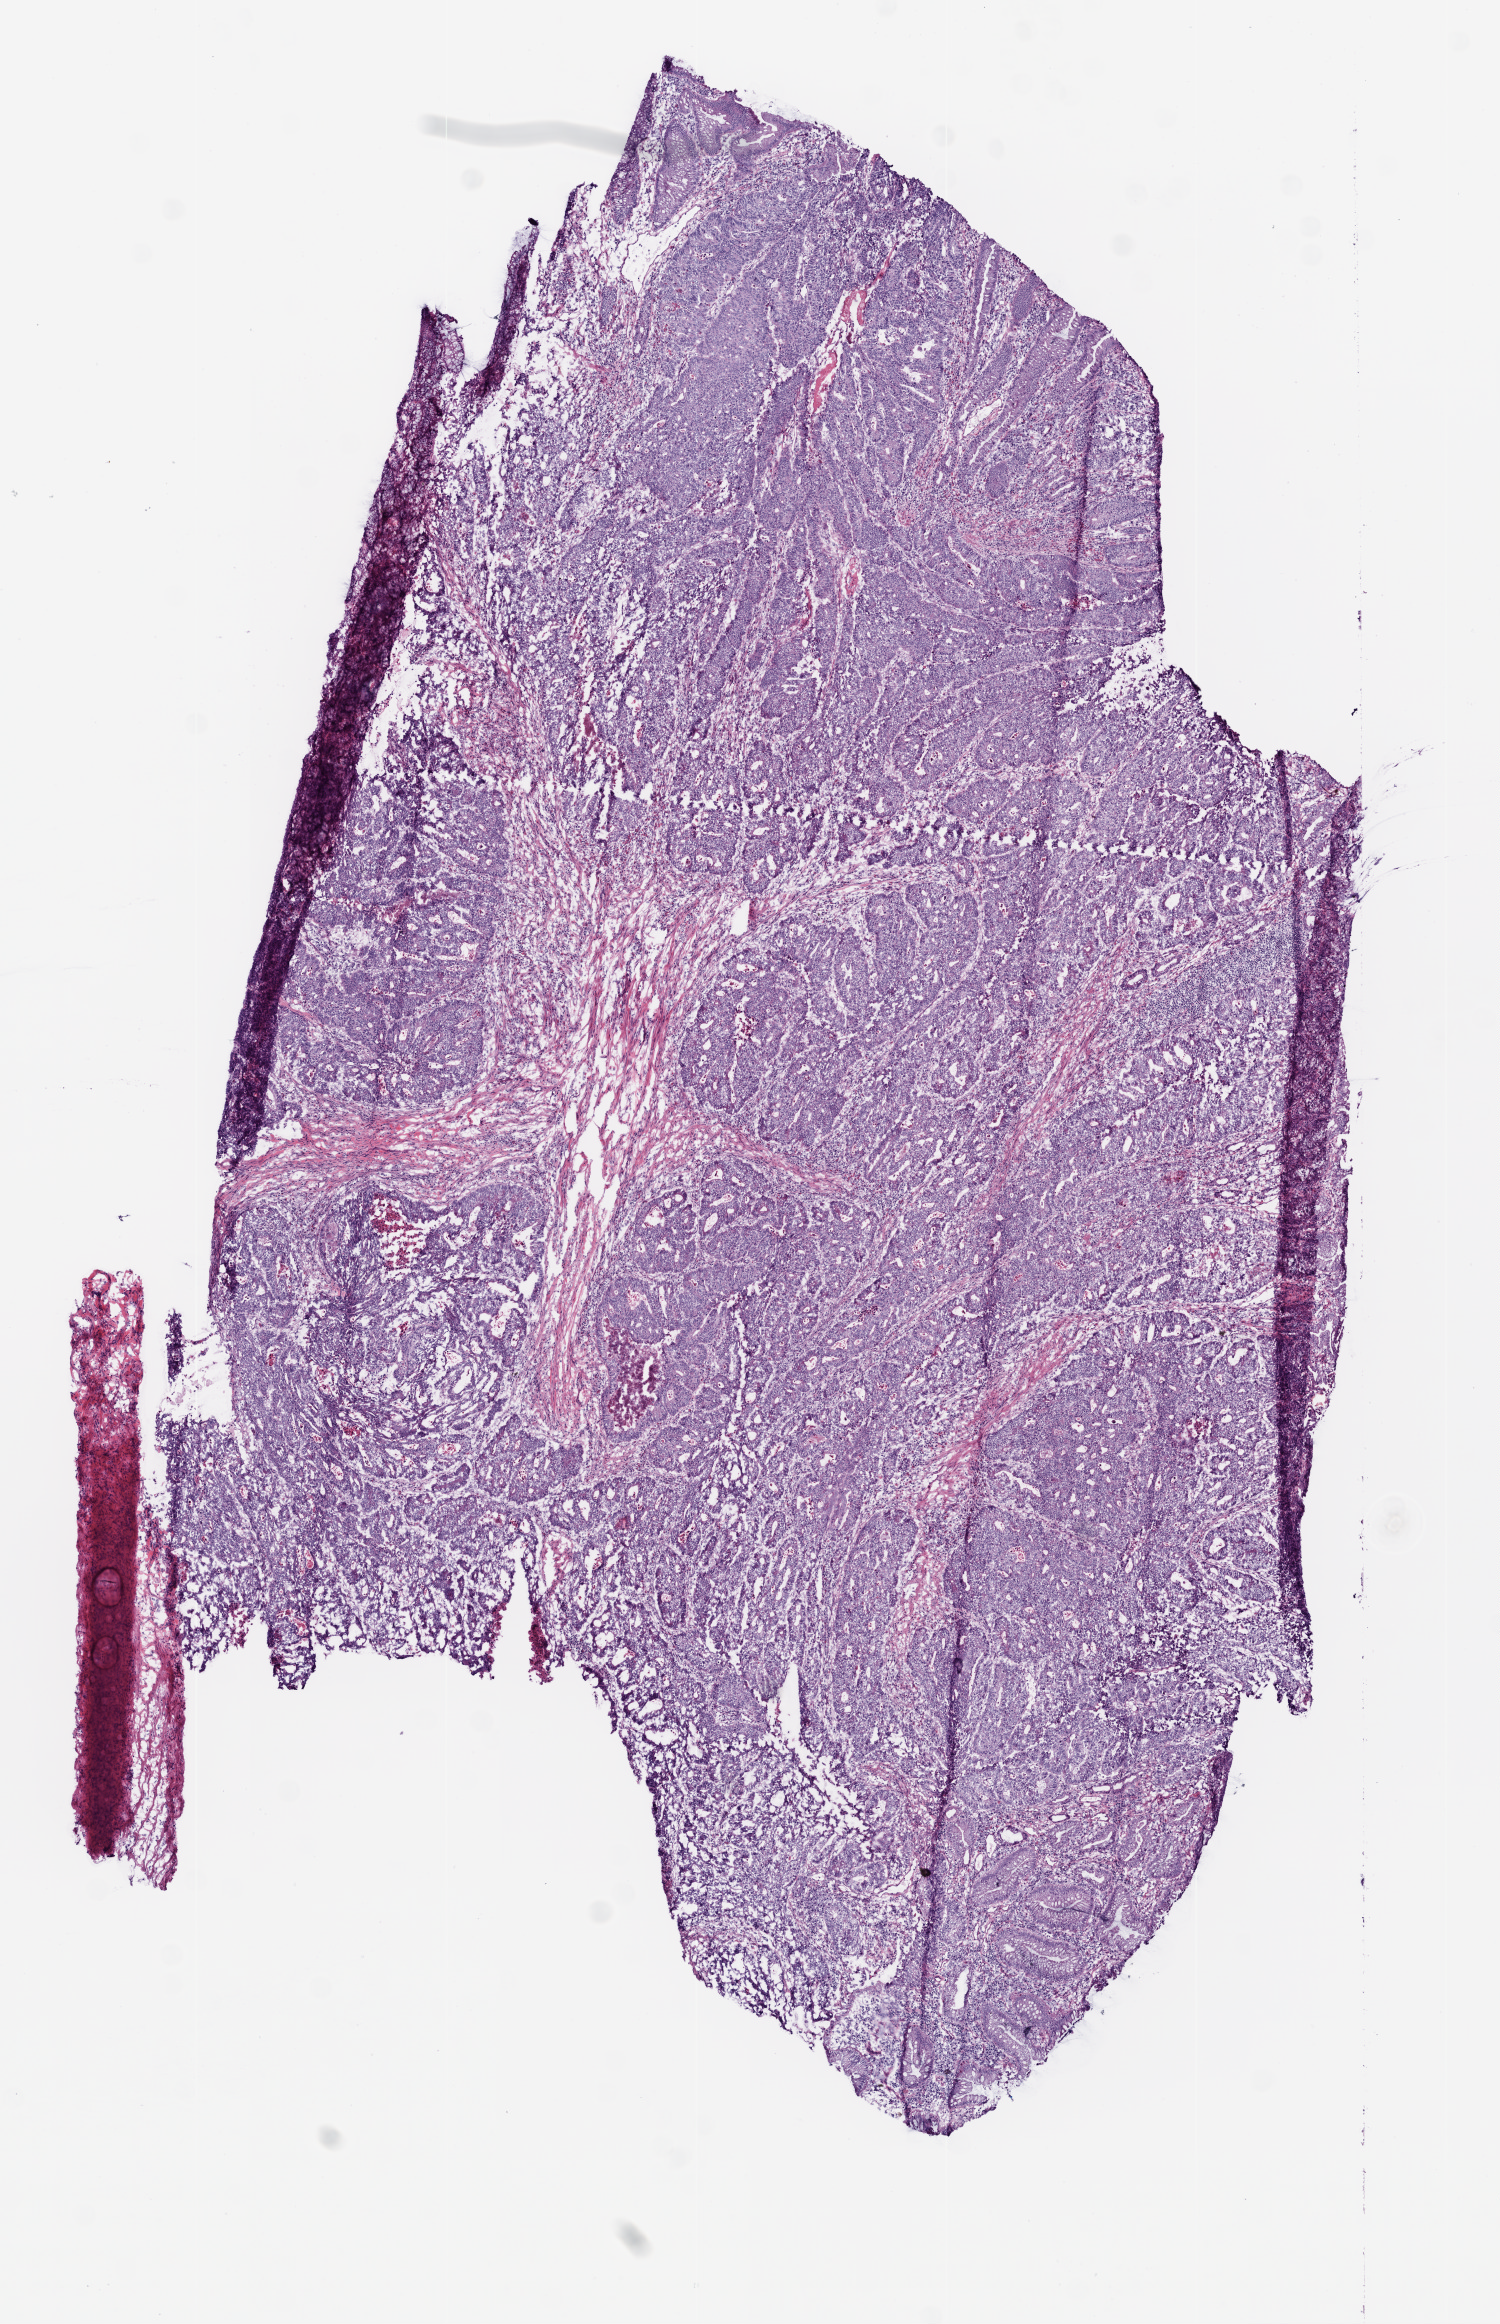
Hematoxylin and eosin (H&E) stained whole-slide image, low-resolution overview of the scanned area, about 6.0 x 9.3 mm (acquisition: 20x scan), frozen section, primary tumour sample from the colon. Male patient; age at initial diagnosis 58 years. Slide review estimates, as recorded: tumour cells 90%, tumour nuclei 95%, normal cells 0%, stromal cells 5%, necrosis 5%.
TNM: T3 N1 M0. AJCC pathologic stage: III. Histologic diagnosis: Adenocarcinoma, NOS. Lymph nodes positive (case pathology): 2 of 19 examined.